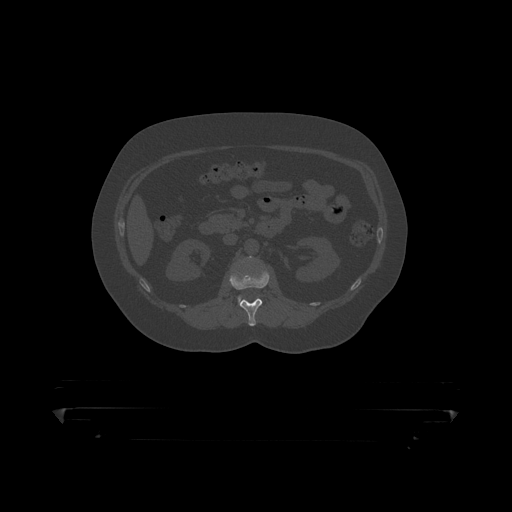
CT including the spine, one axial slice. Slice 135 of 390 in the series (ordered by position). Reconstruction kernel STANDARD. Bone window (W 1800 / L 400 HU). 512 × 512 image matrix, field of view 650 × 650 mm. Male patient, age 60 years. Case-level facts recorded for this patient, not image findings: primary cancer: prostate.
Outlined on this slice (semi-automatically segmented with operator editing):
- L1 vertebra: bounding box (x1, y1, x2, y2) in pixels: (230, 269, 270, 319)
- L2 vertebra: (238, 257, 254, 304)